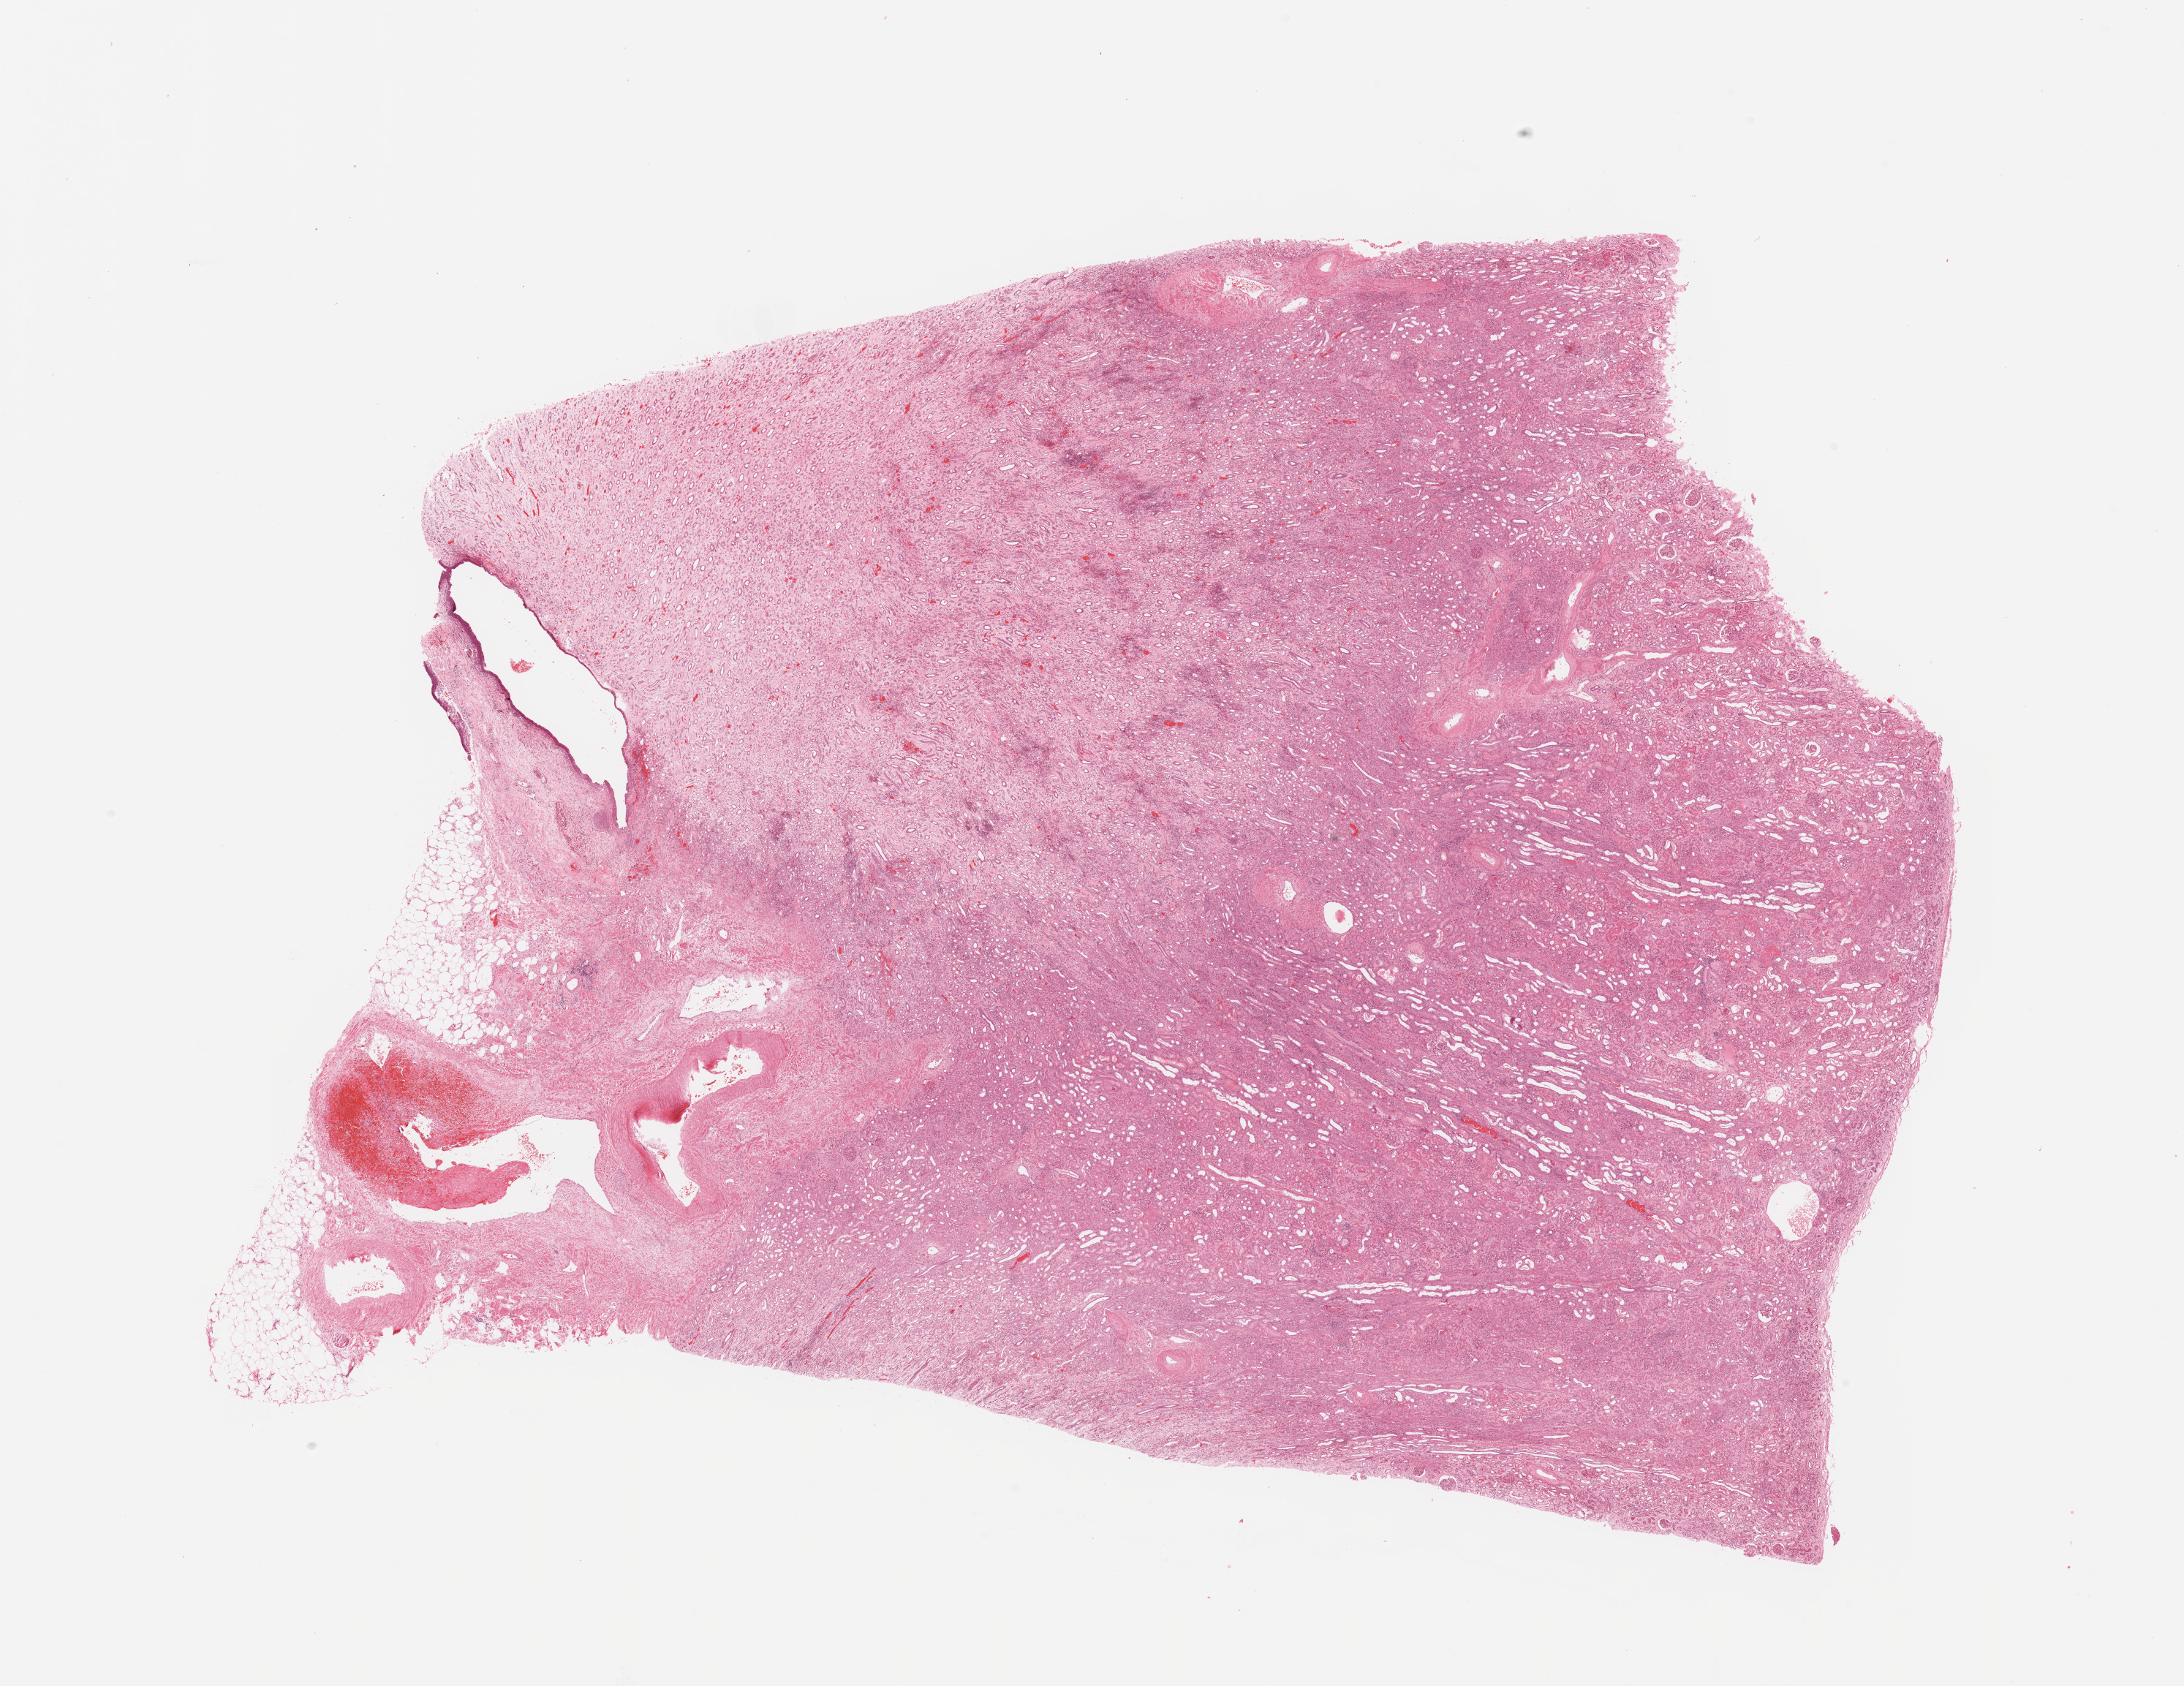
Whole-slide histology image, Hematoxylin and eosin (H&E) stained — whole scanned area (about 23.6 x 18.2 mm, acquisition: 20x scan) shown as a low-resolution overview, normal (non-tumour) tissue sample, sampled site: kidney. Patient: male, age 60 years.
This section: normal (non-tumour) tissue from the same patient. Patient diagnosis: Renal cell carcinoma, NOS.